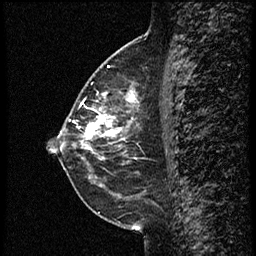
Breast MRI (dynamic contrast-enhanced), one sagittal slice. Slice 27 of 60 in the series (ordered by position). Dynamic contrast-enhanced study with each time point stored as its own series, time point 2 of 3 at this slice position (early post-contrast, ordered by acquisition time). 1.5 T. TE 4.2 ms, TR 18.9 ms. 2 mm slice thickness. 256 × 256 image matrix, field of view 200 × 200 mm. Female patient. Case-level facts recorded for this patient, not image findings: setting: breast cancer imaged before/during neoadjuvant chemotherapy; receptor status: HER2-positive.
Outlined on this slice (semi-automatically segmented with operator editing):
- analysis volume of interest (the breast-tissue region the enhancement analysis was run in; not a lesion): bounding box <77,83,151,147> (left, top, right, bottom; pixels)
- tumour enhancement mask (voxels above the 100 % enhancement threshold inside the analysis volume of interest): <77,89,138,147>